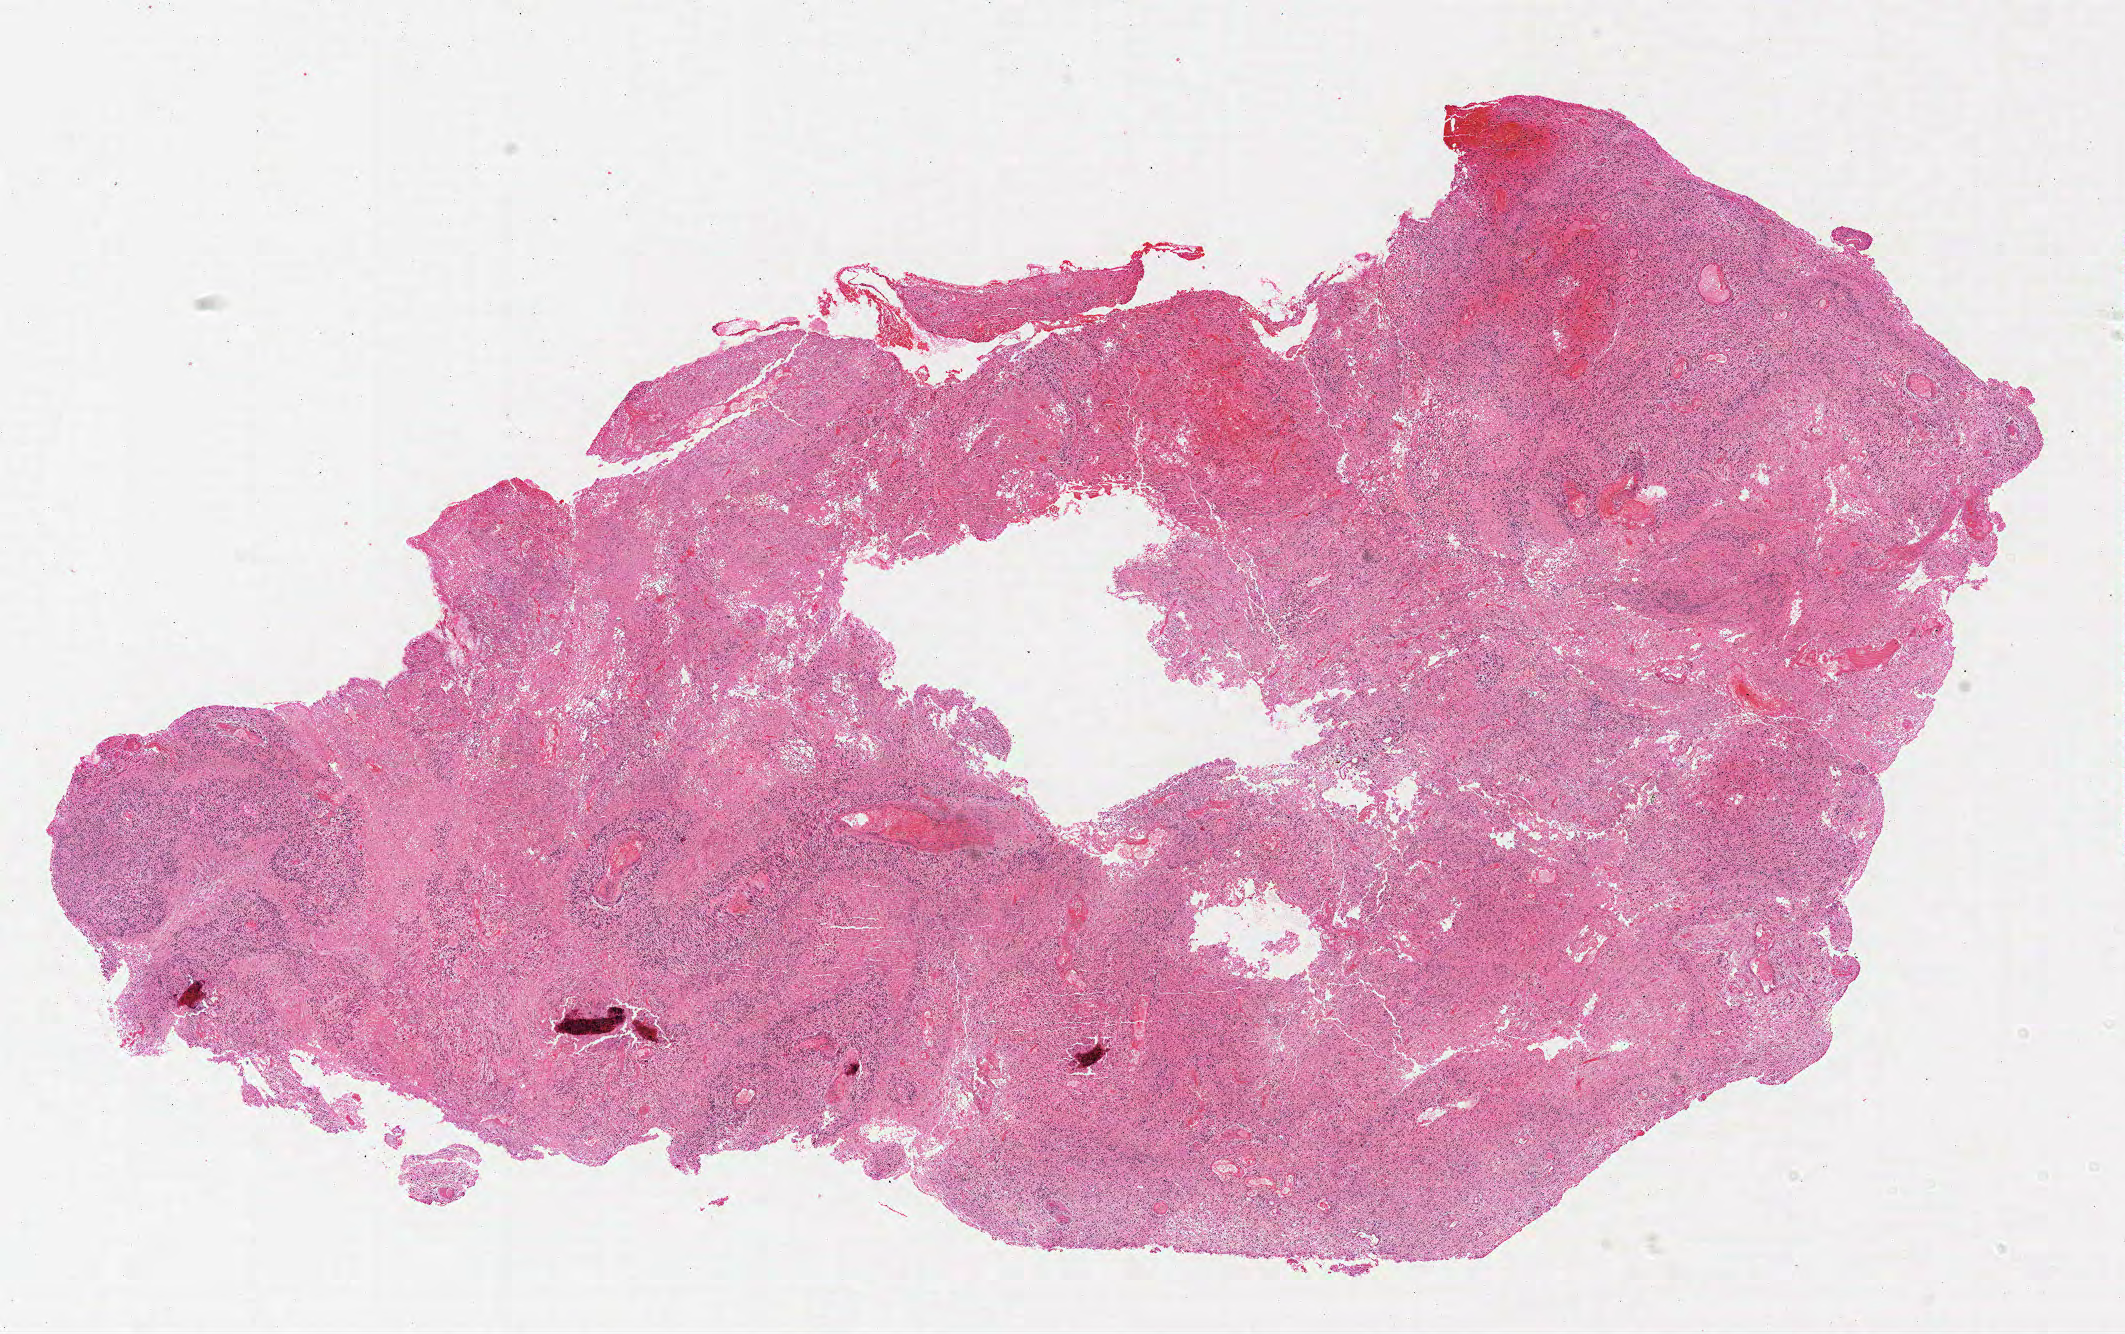
H&E whole-slide image — whole scanned area (about 17.0 x 10.7 mm, slide scanned at 20x) shown as a low-resolution overview, formalin-fixed paraffin-embedded (FFPE) diagnostic section, sample: primary tumour, brain. Female, age 53 years at initial diagnosis.
Diagnosis: Glioblastoma.